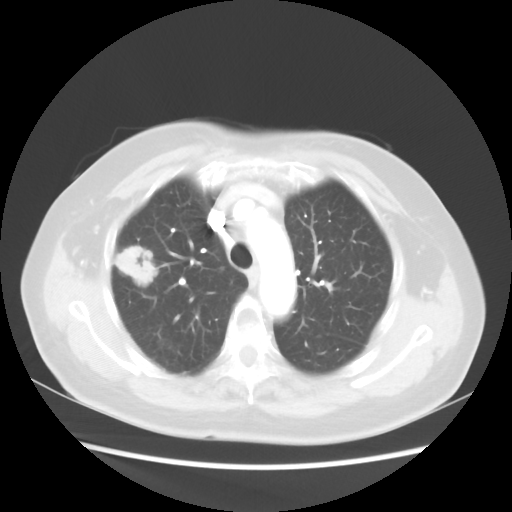
Chest CT, one axial slice. Position 35 of 48 along the scan axis. Reconstruction kernel STANDARD. 100 kVp. Lung window (W 1500 / L -600 HU). 5 mm slice thickness. 512 × 512 image matrix. Patient: female, 75 years. Case-level facts recorded for this patient, not image findings: clinical TNM (as recorded): T1c N0 M0.
Outlined on this slice (rectangle marked by the reading radiologist):
- lung tumour (recorded histology: adenocarcinoma): bounding box [x1, y1, x2, y2] px = [114, 242, 160, 286]